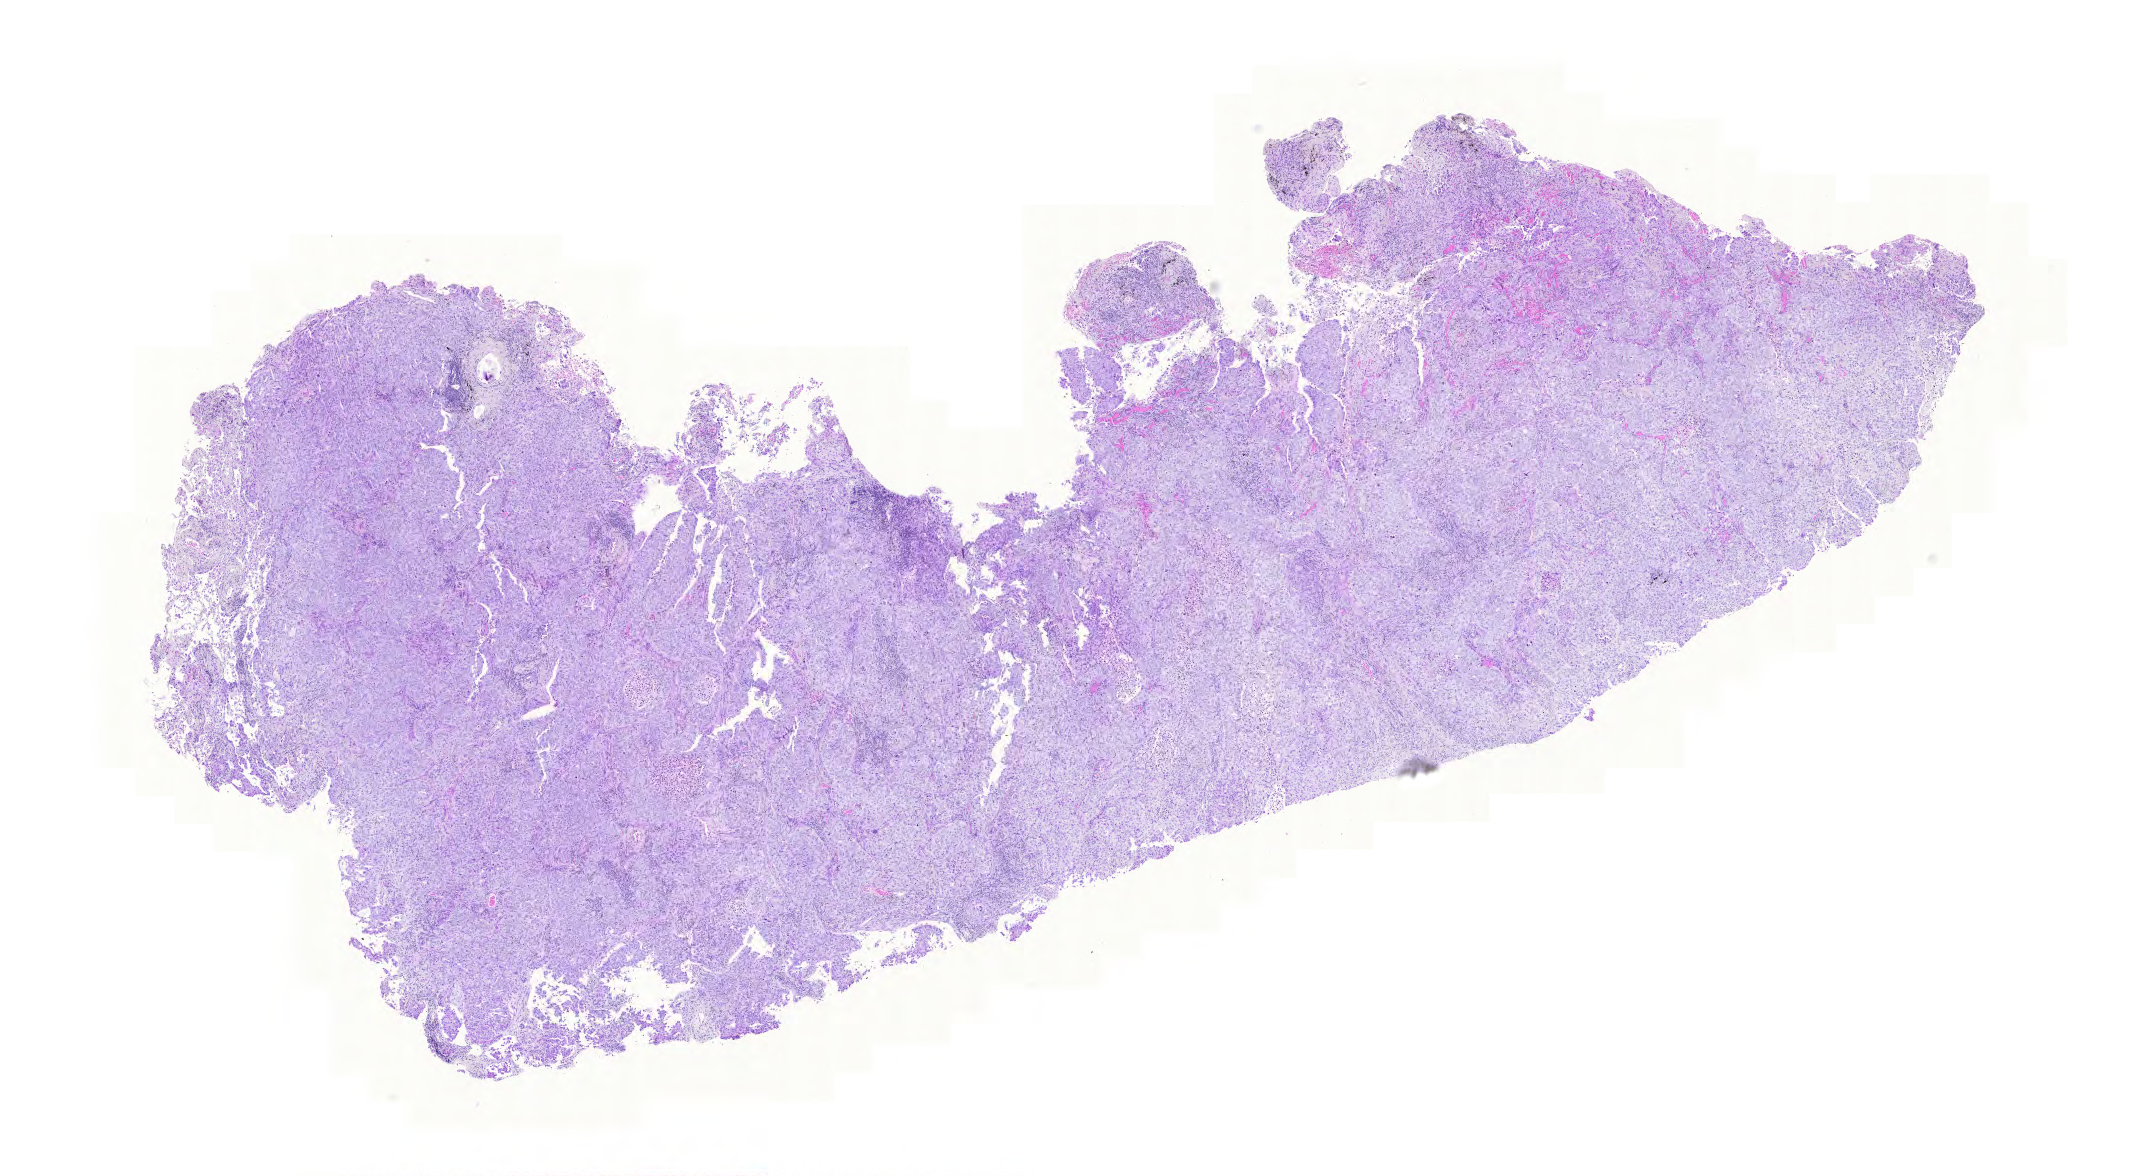
Digitized H&E tissue section (whole slide), shown as a low-resolution overview of the whole scanned area (about 16.0 x 8.7 mm, from a 20x scan); FFPE section; primary tumour sample from the lung. Female patient; age at initial diagnosis 79 years.
• TNM: T3 N1 M0
• AJCC pathologic stage: IIIA (6th edition)
• pathologic diagnosis: Adenocarcinoma, NOS (lower lobe, lung)